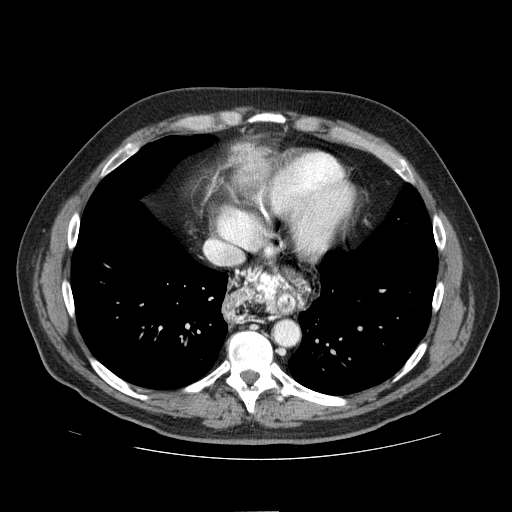
Contrast-enhanced abdominal CT (liver protocol), one axial slice. Position 70 of 81 along the scan axis. Reconstruction kernel STANDARD. 100 kVp. One of 2 acquisitions stored at this slice position. Soft-tissue window (W 400 / L 40 HU). 2.5 mm slice thickness. 512 × 512 image matrix, field of view 400 × 400 mm. Case-level facts recorded for this patient, not image findings: diagnosis: hepatocellular carcinoma (patient treated with transarterial chemoembolisation; whether this scan precedes or follows treatment is not stated here); TNM stage (as recorded): Stage-IIIA; Child-Pugh class: A; tumour nodularity: multinodular; tumour size: 5.6 cm.
Outlined on this slice (semi-automatically segmented with operator editing):
- mass: box from (x=233, y=143) to (x=270, y=181) px